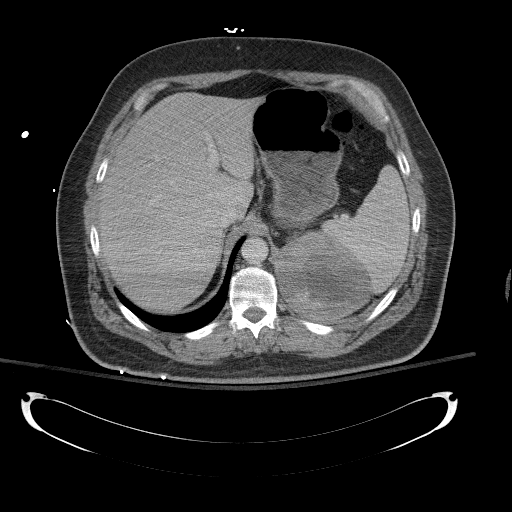
Contrast-enhanced abdominal CT, one axial slice. Position 94 of 154 along the scan axis. Reconstruction kernel B41f. Intravenous contrast given. Soft-tissue window (W 400 / L 40 HU). 5 mm slice thickness. 512 × 512 image matrix, field of view 467 × 467 mm. Patient: male, 43 years. Case-level facts recorded for this patient, not image findings: diagnosis: adrenocortical carcinoma; tumour side: left adrenal; tumour size at pathology: 9.8 cm; Ki-67 index: 30 %; stage (as recorded): 2.
Structures marked on this image (semi-automatic segmentation, software-assisted and operator-edited):
- mass: bounding box (x1, y1, x2, y2) in pixels: (281, 232, 366, 319)